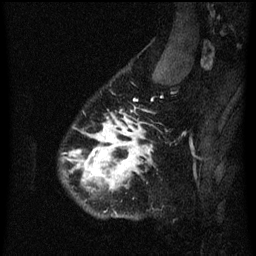
Breast MRI (dynamic contrast-enhanced), one sagittal slice; slice 52 of 60 in the series (ordered by position); dynamic contrast-enhanced series, image 2 of 3 at this slice position (ordered by acquisition); 1.5 T; TE 4.2 ms, TR 8.4 ms; 256 × 256 image matrix, field of view 180 × 180 mm. Female patient, age 34 years. Case-level facts recorded for this patient, not image findings: setting: breast cancer imaged before/during neoadjuvant chemotherapy; receptor status: HR-positive, HER2-negative.
Annotated regions visible in this slice (semi-automatic segmentation, software-assisted and operator-edited):
- analysis volume of interest (the breast-tissue region the enhancement analysis was run in; not a lesion): bounding box <62,58,173,221> (left, top, right, bottom; pixels)
- tumour enhancement mask (voxels above the 70 % enhancement threshold inside the analysis volume of interest): <70,118,153,191>